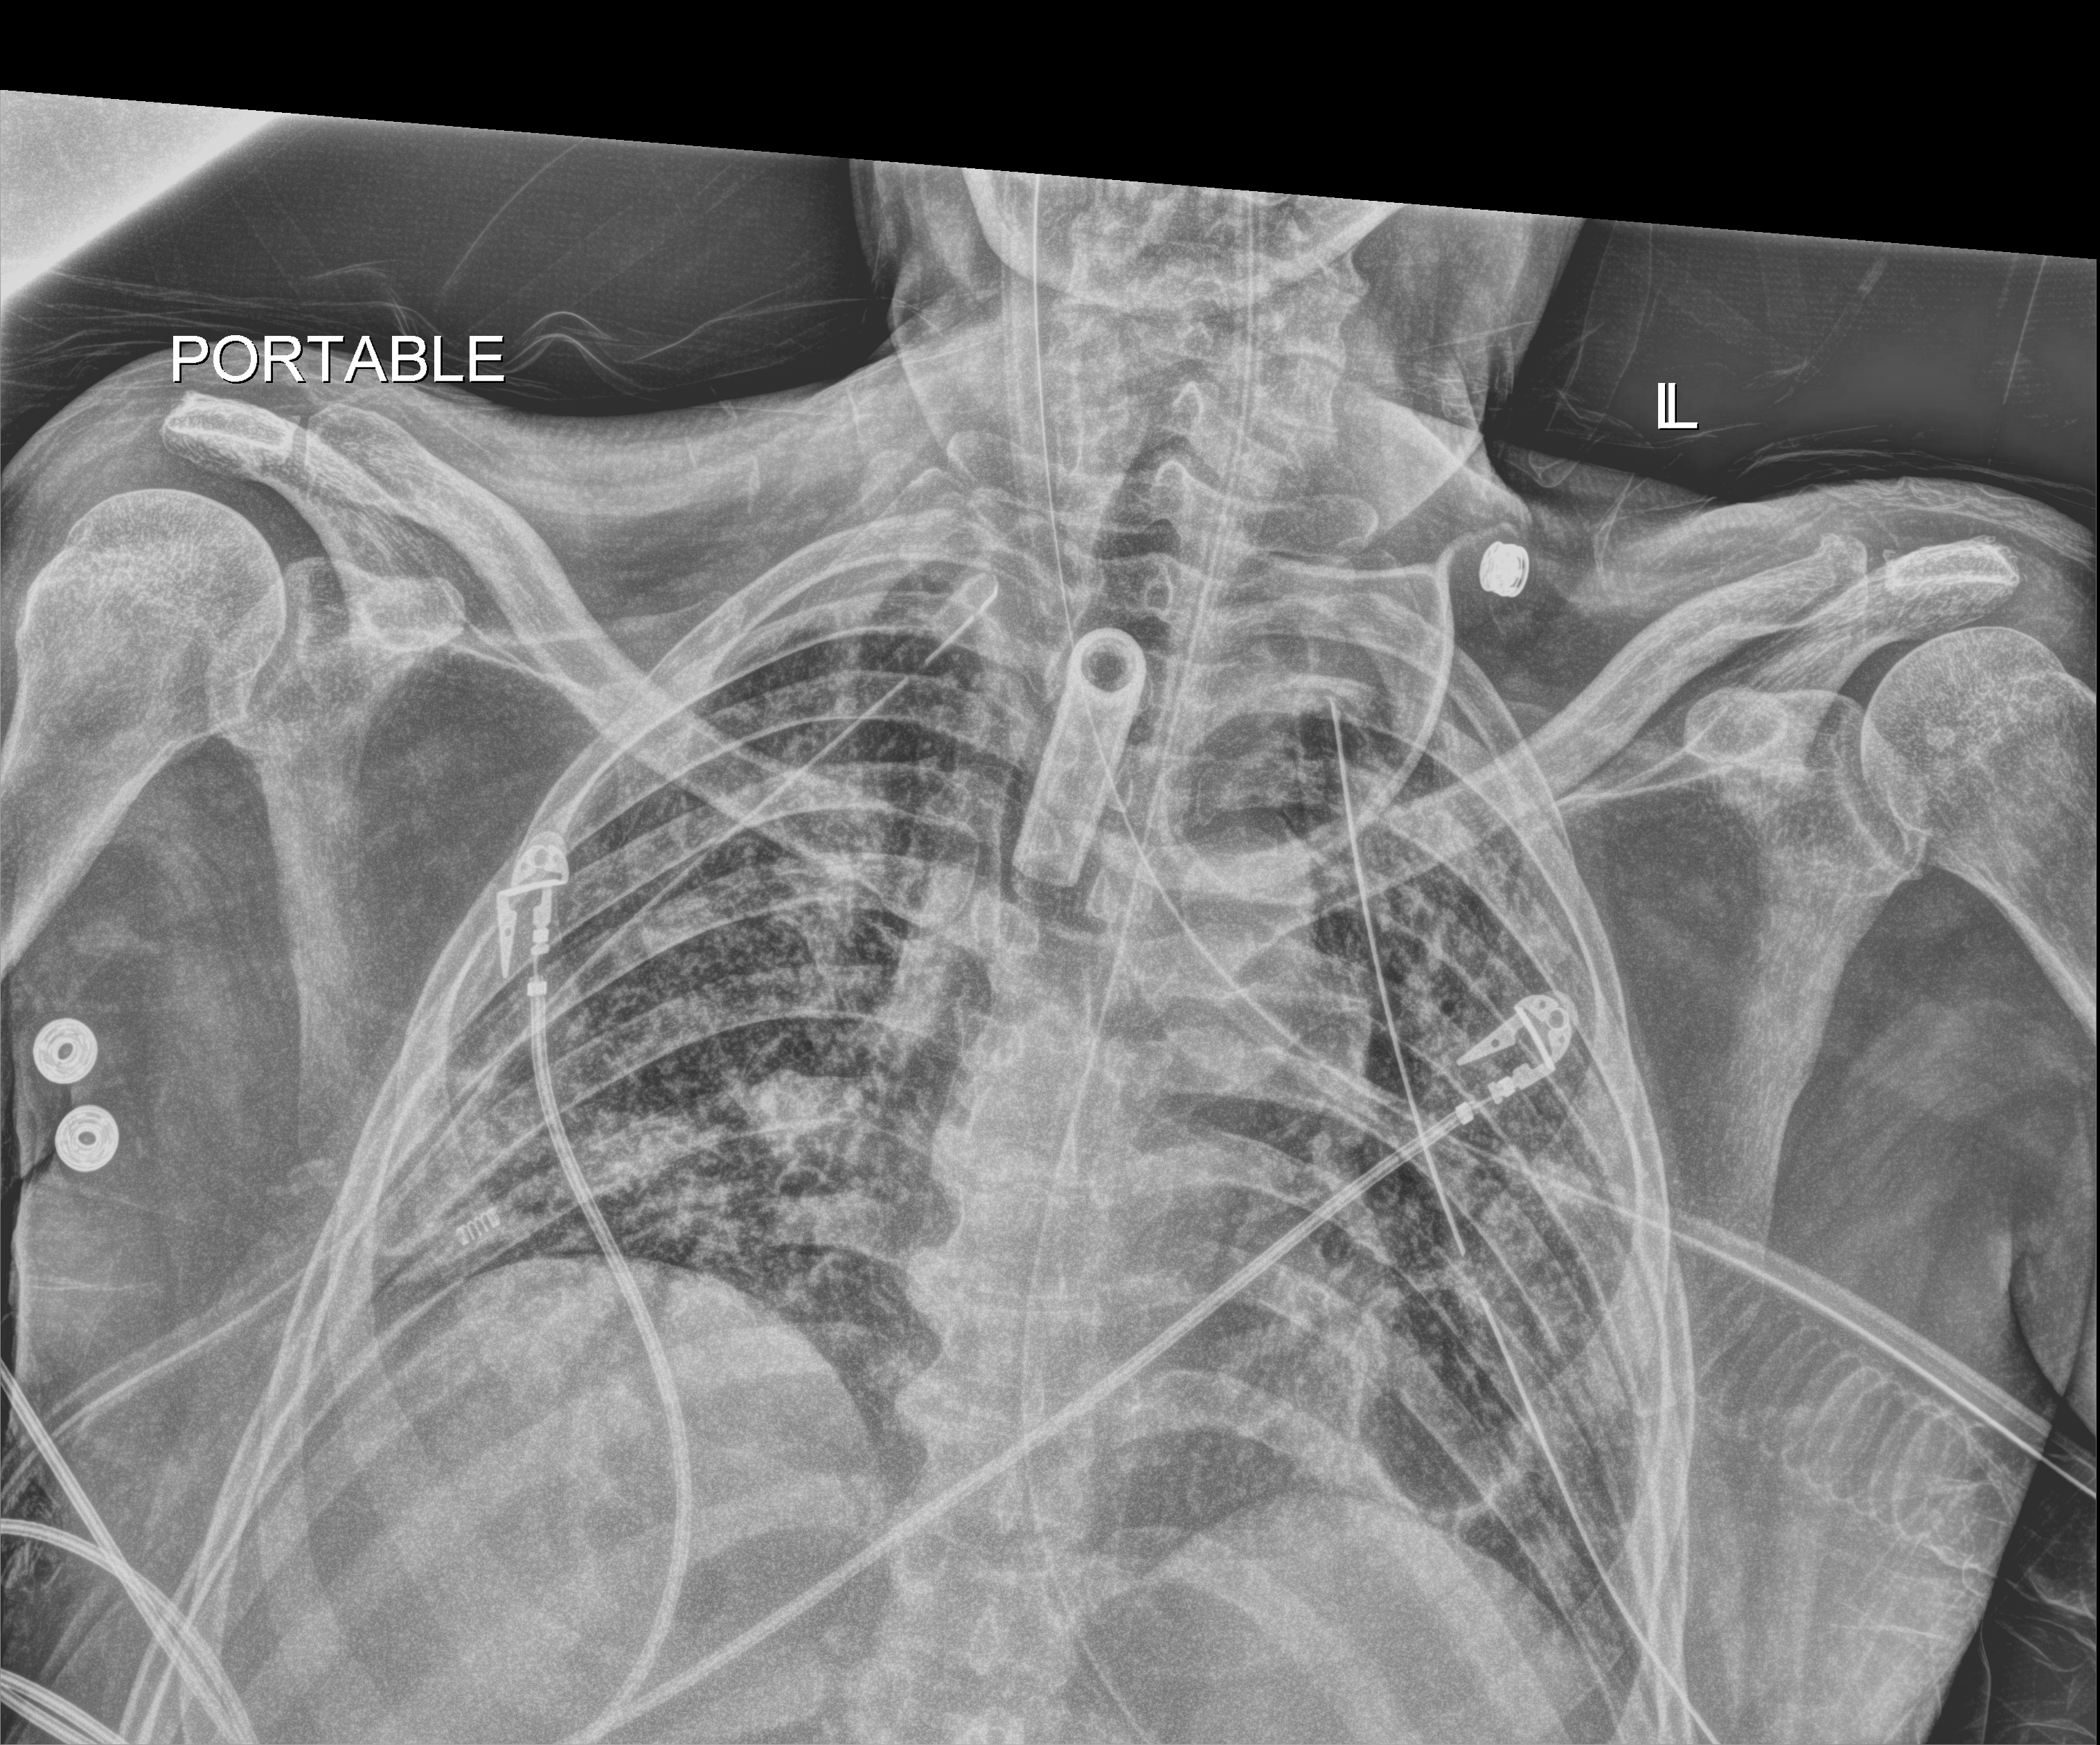
Chest X-ray (portable), anteroposterior (AP) projection. Male patient hospitalised with COVID-19, age 18–59 years.
Hospital-stay facts (about this admission, not read from this image; timing relative to this image not recorded): other chronic lung disease (admission record): no; mechanically ventilated during this hospital stay: yes; admitted to intensive care during this hospital stay: yes.